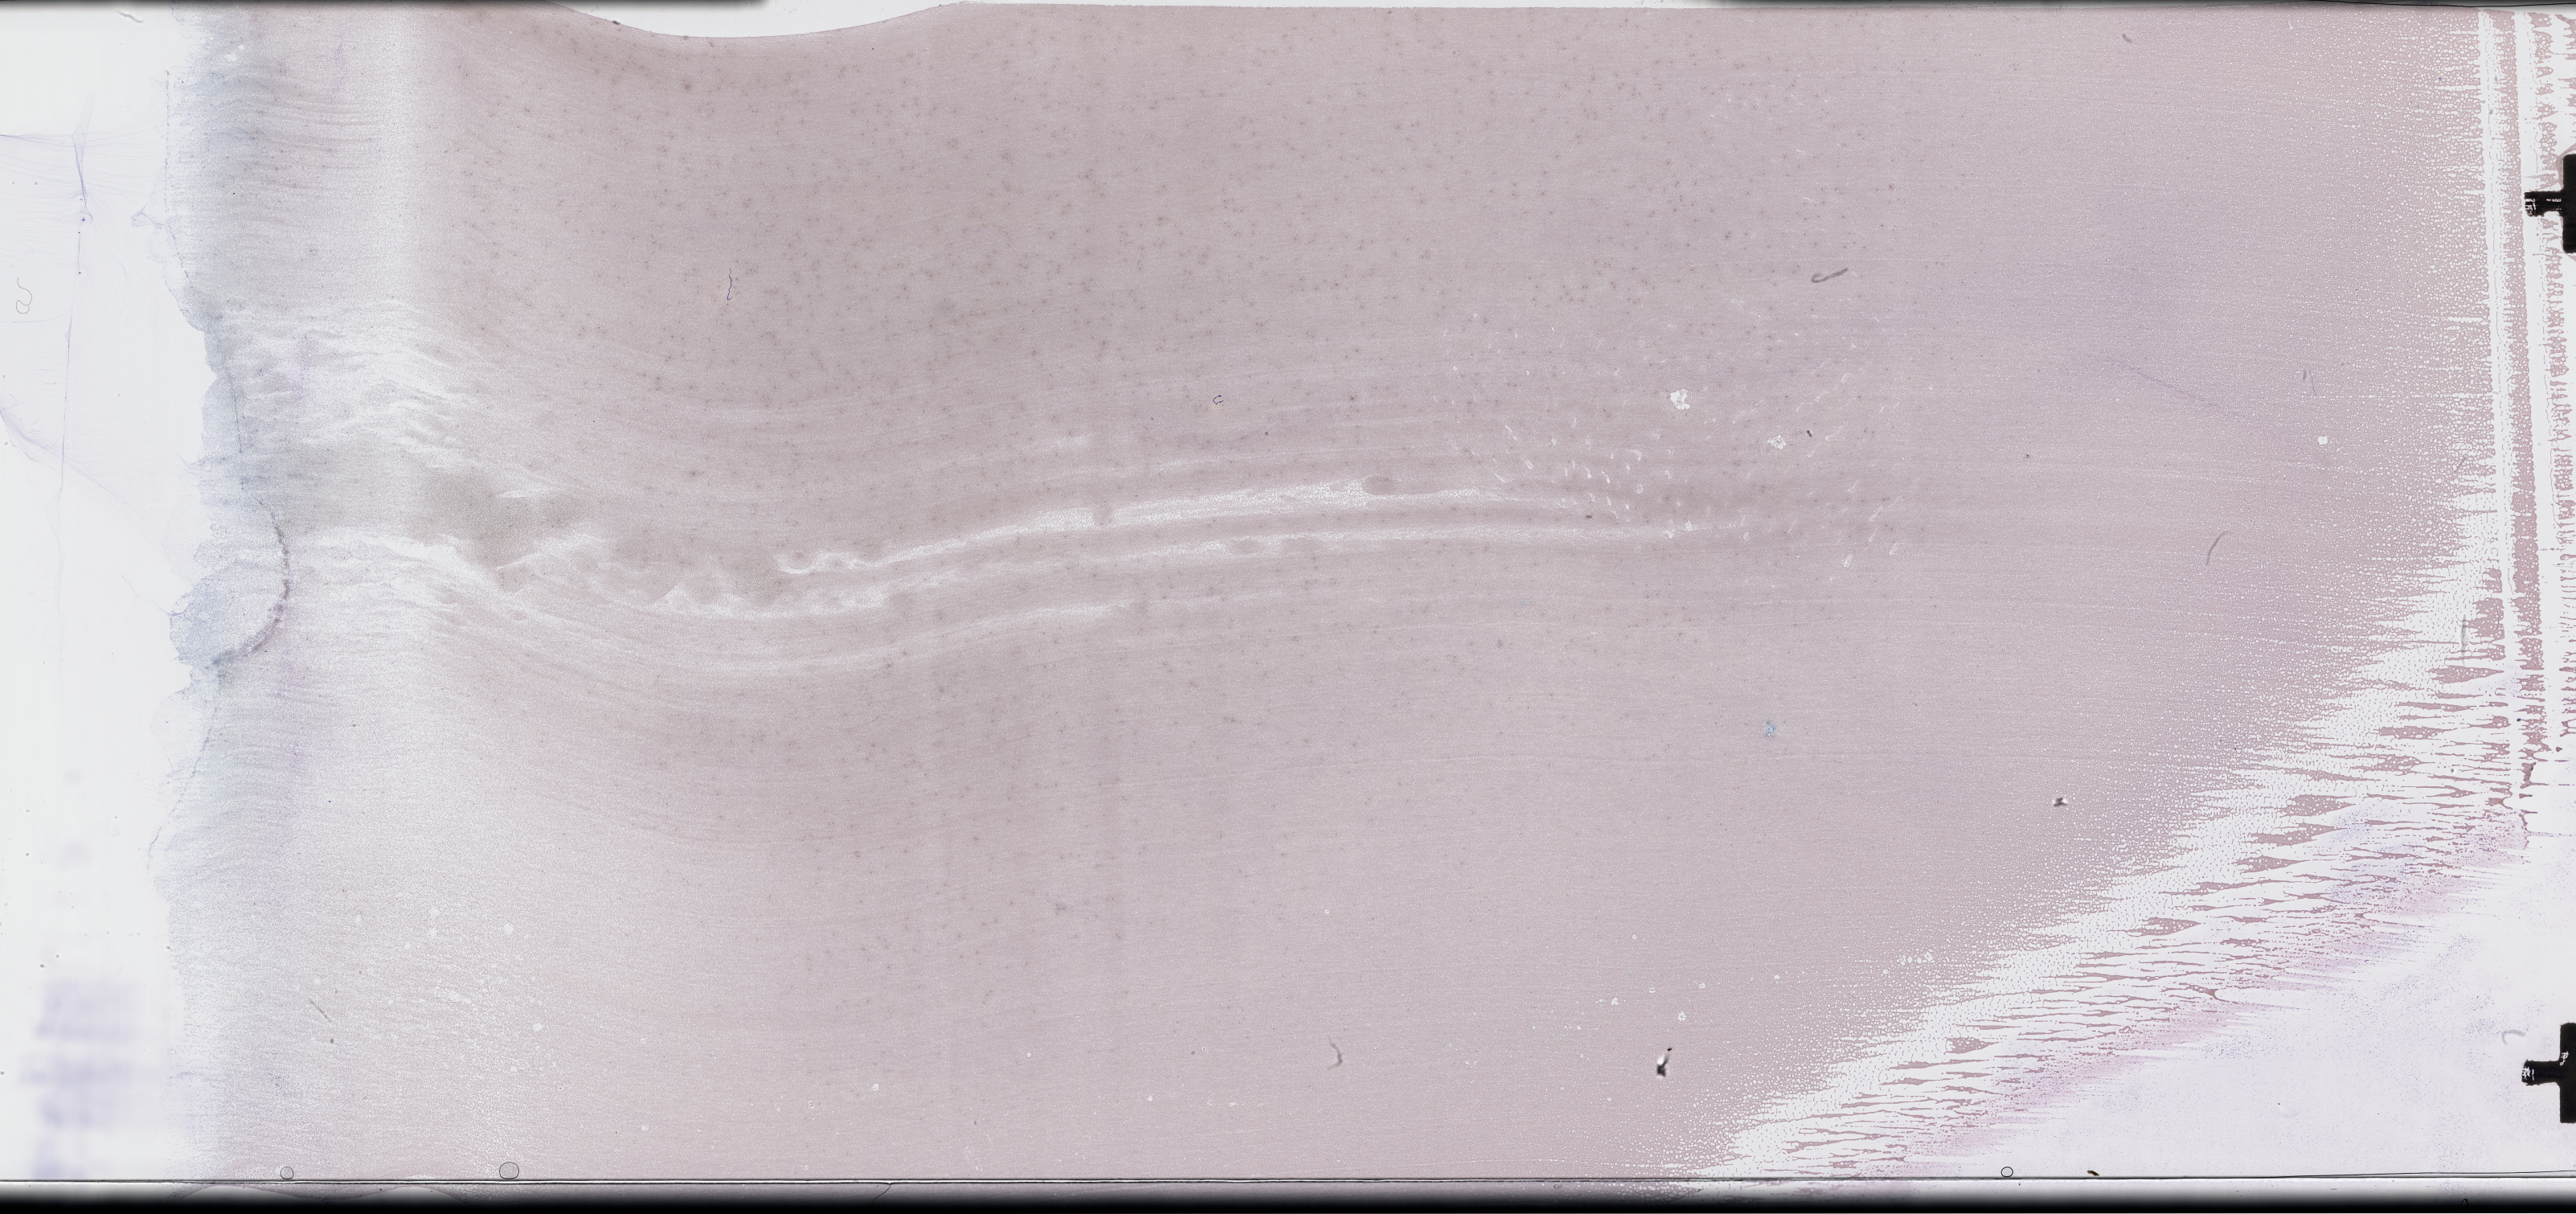
Wright–Giemsa-stained whole blood smear, whole-slide image, low-resolution overview of the scanned area, about 51.8 x 24.4 mm. EDTA-anticoagulated smear. Patient sex: male.
From a patient with: Plasma Cell Myeloma.